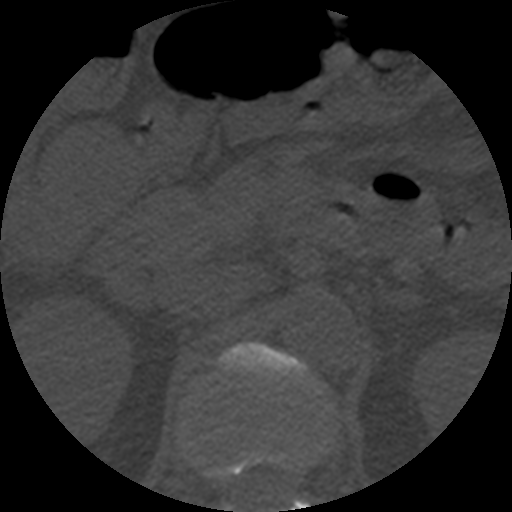
CT including the spine, one axial slice; slice 200 of 508 in the series (ordered by position); 120 kVp; bone window (W 1800 / L 400 HU); 1.25 mm slice thickness; 512 × 512 image matrix, field of view 160 × 160 mm. Patient age 57 years. Case-level facts recorded for this patient, not image findings: primary cancer: prostate.
Outlined on this slice (semi-automatic segmentation, software-assisted and operator-edited):
- L1 vertebra: box from (x=218, y=343) to (x=309, y=512) px
- T12 vertebra: (x=229, y=450)–(x=302, y=473)